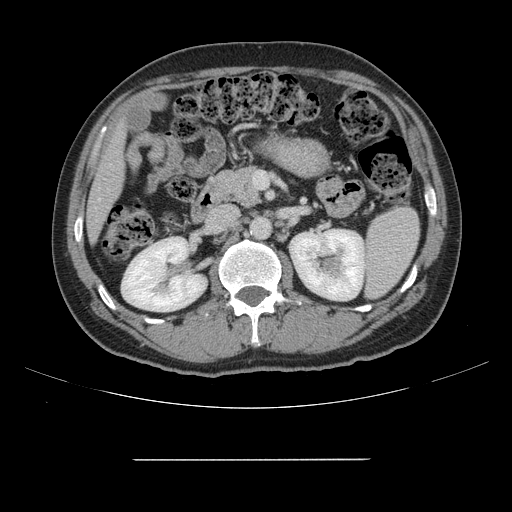
Contrast-enhanced abdominal CT, one axial slice; slice 63 of 164 in the series (ordered by position); 120 kVp; soft-tissue window (W 400 / L 40 HU); 512 × 512 image matrix. Male patient, age 54 years. Case-level facts recorded for this patient, not image findings: diagnosis: colorectal cancer liver metastases, imaged before liver resection; multiple liver metastases: yes; largest metastasis: 1 cm; disease in both lobes: no.
Annotated regions visible in this slice (manually delineated by an expert):
- liver: bounding box <88,129,124,237> (left, top, right, bottom; pixels)
- planned liver remnant (the part of the liver to remain after resection): <88,129,124,237>